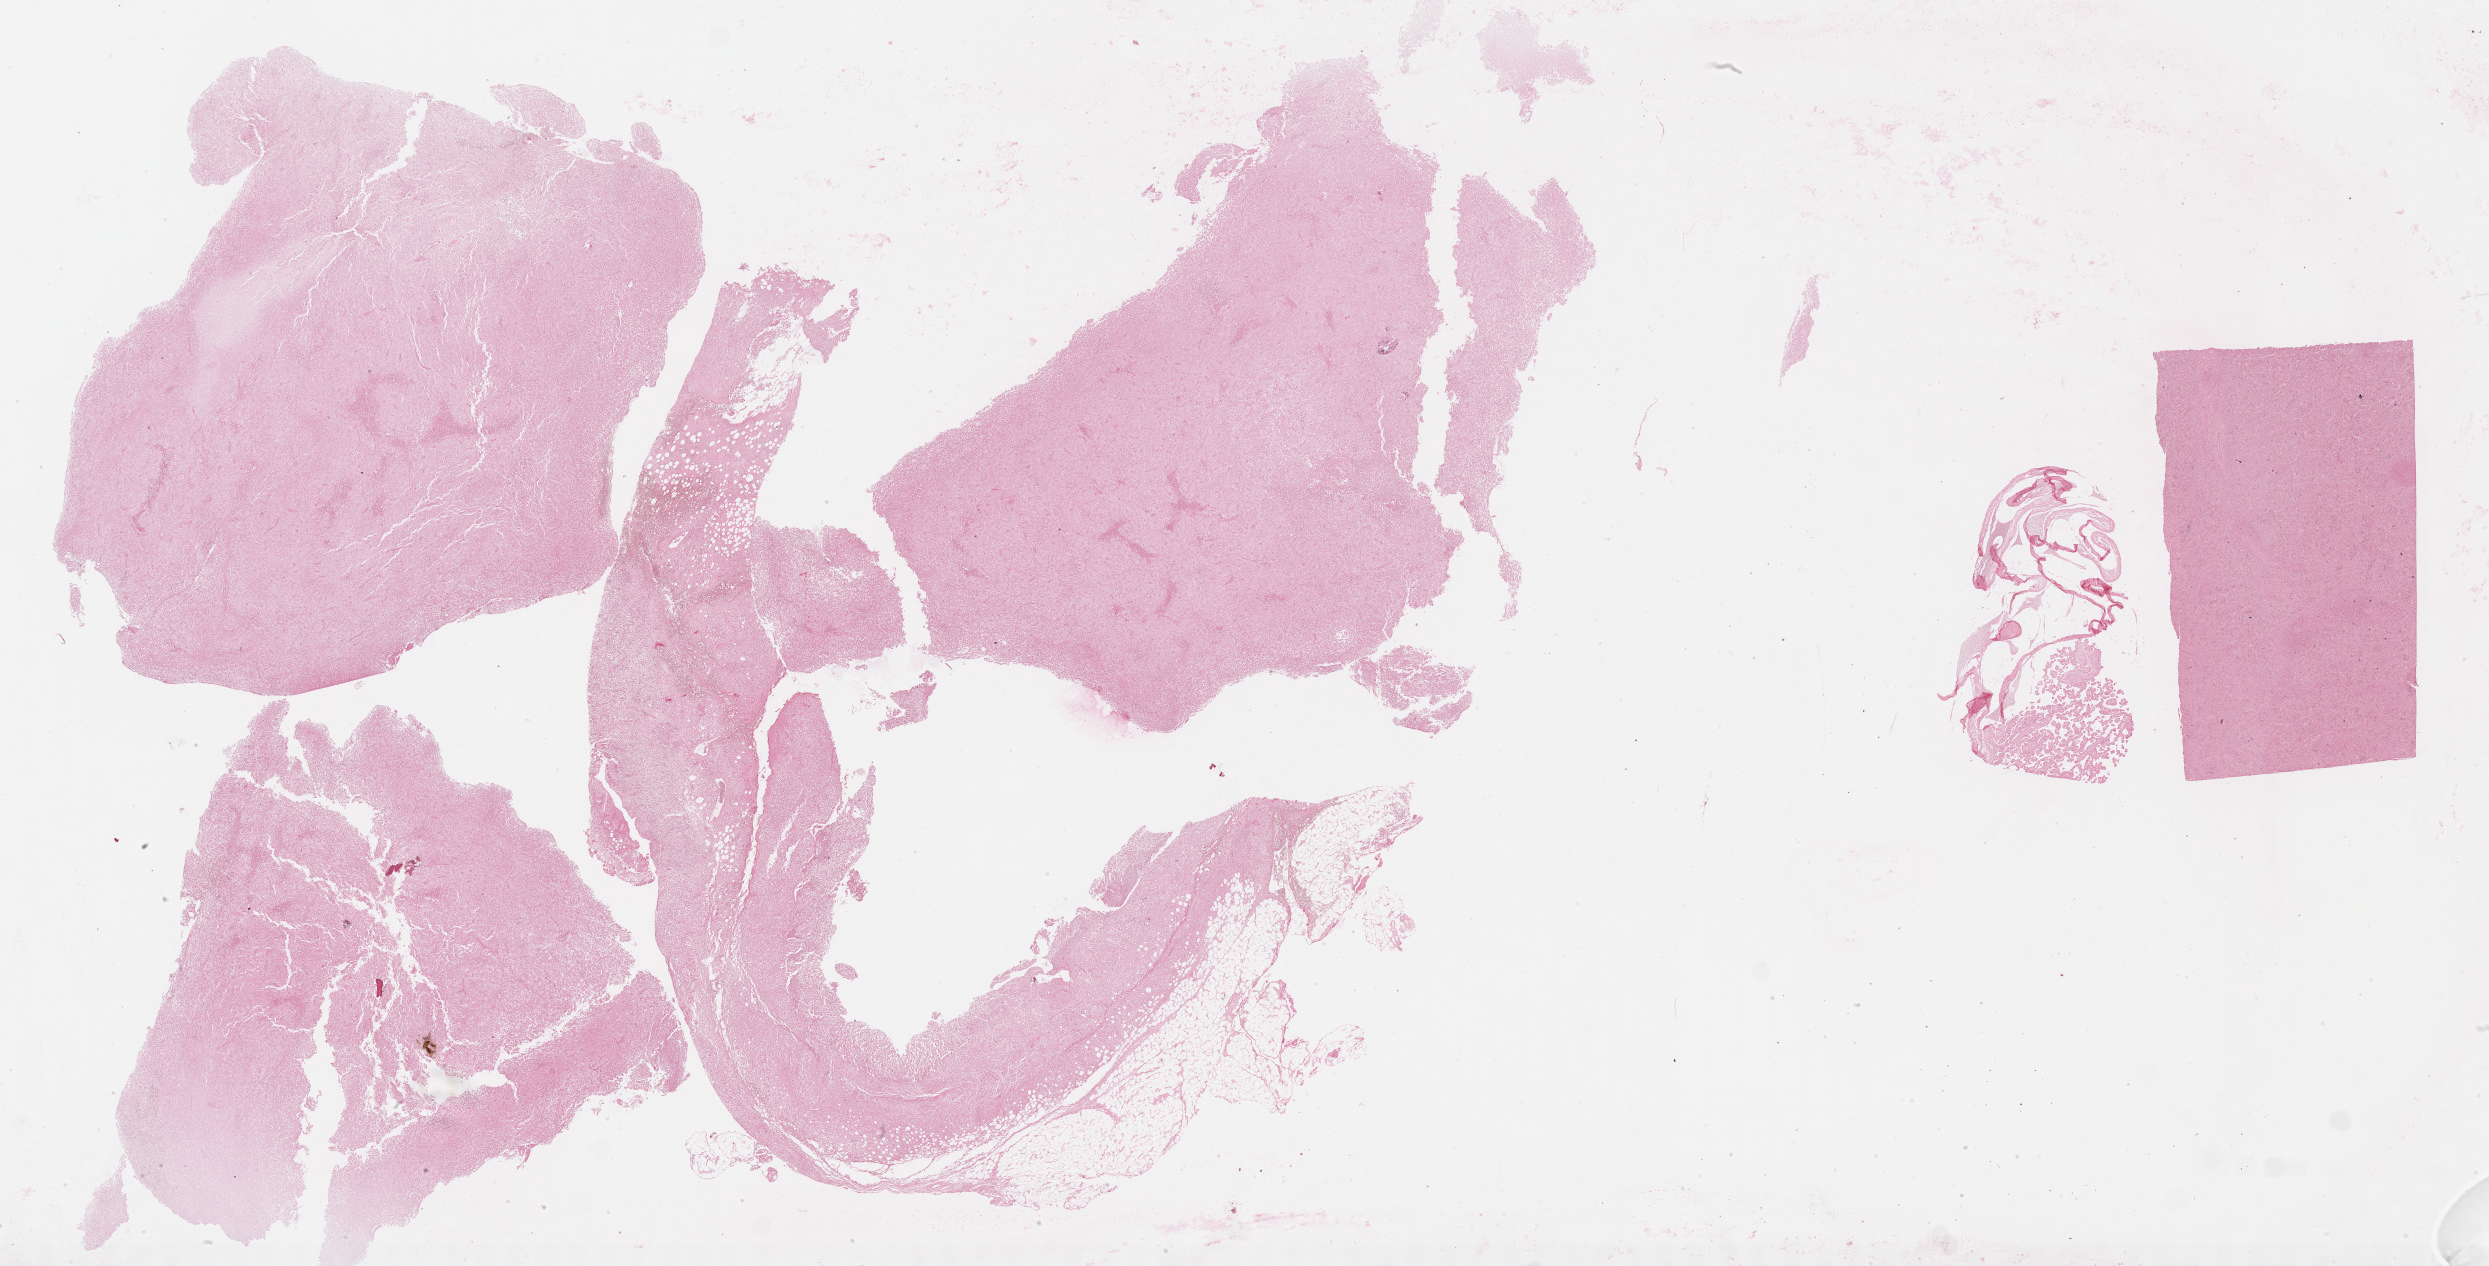
Whole-slide image, Epstein–Barr virus-encoded RNA (EBER) in-situ hybridisation — shown as a low-resolution overview of the whole scanned area (about 40.3 x 20.5 mm). Patient sex: female.
Specimen: tumor tissue.